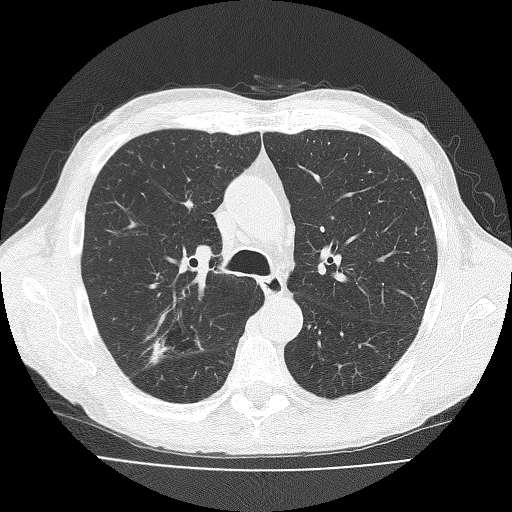
Chest CT (low-dose screening protocol), one axial image; third screening round (two years after baseline); lung window (W 1500 / L -600 HU); 2 mm slice thickness; lung (sharp) reconstruction kernel (FC51); 120 kVp; slice 63 of 181 in the series. Male participant, aged 73 years at enrolment. Current smoker at enrolment.
Expert-annotated lung lesion, bounding box [x1, y1, x2, y2] px = [139, 321, 193, 378]. Screening reader's record for this exam (one nodule recorded; not confirmed to be the boxed lesion): non-calcified nodule or mass ≥4 mm, right upper lobe, 11 × 10 mm, spiculated (stellate) margins, soft tissue attenuation, pre-existing on the prior screen: no. Lung cancer was diagnosed 38 days after this screen: adenosquamous carcinoma, right upper lobe, well differentiated (G1), stage IA (AJCC 6th edition), 20 mm at pathology.